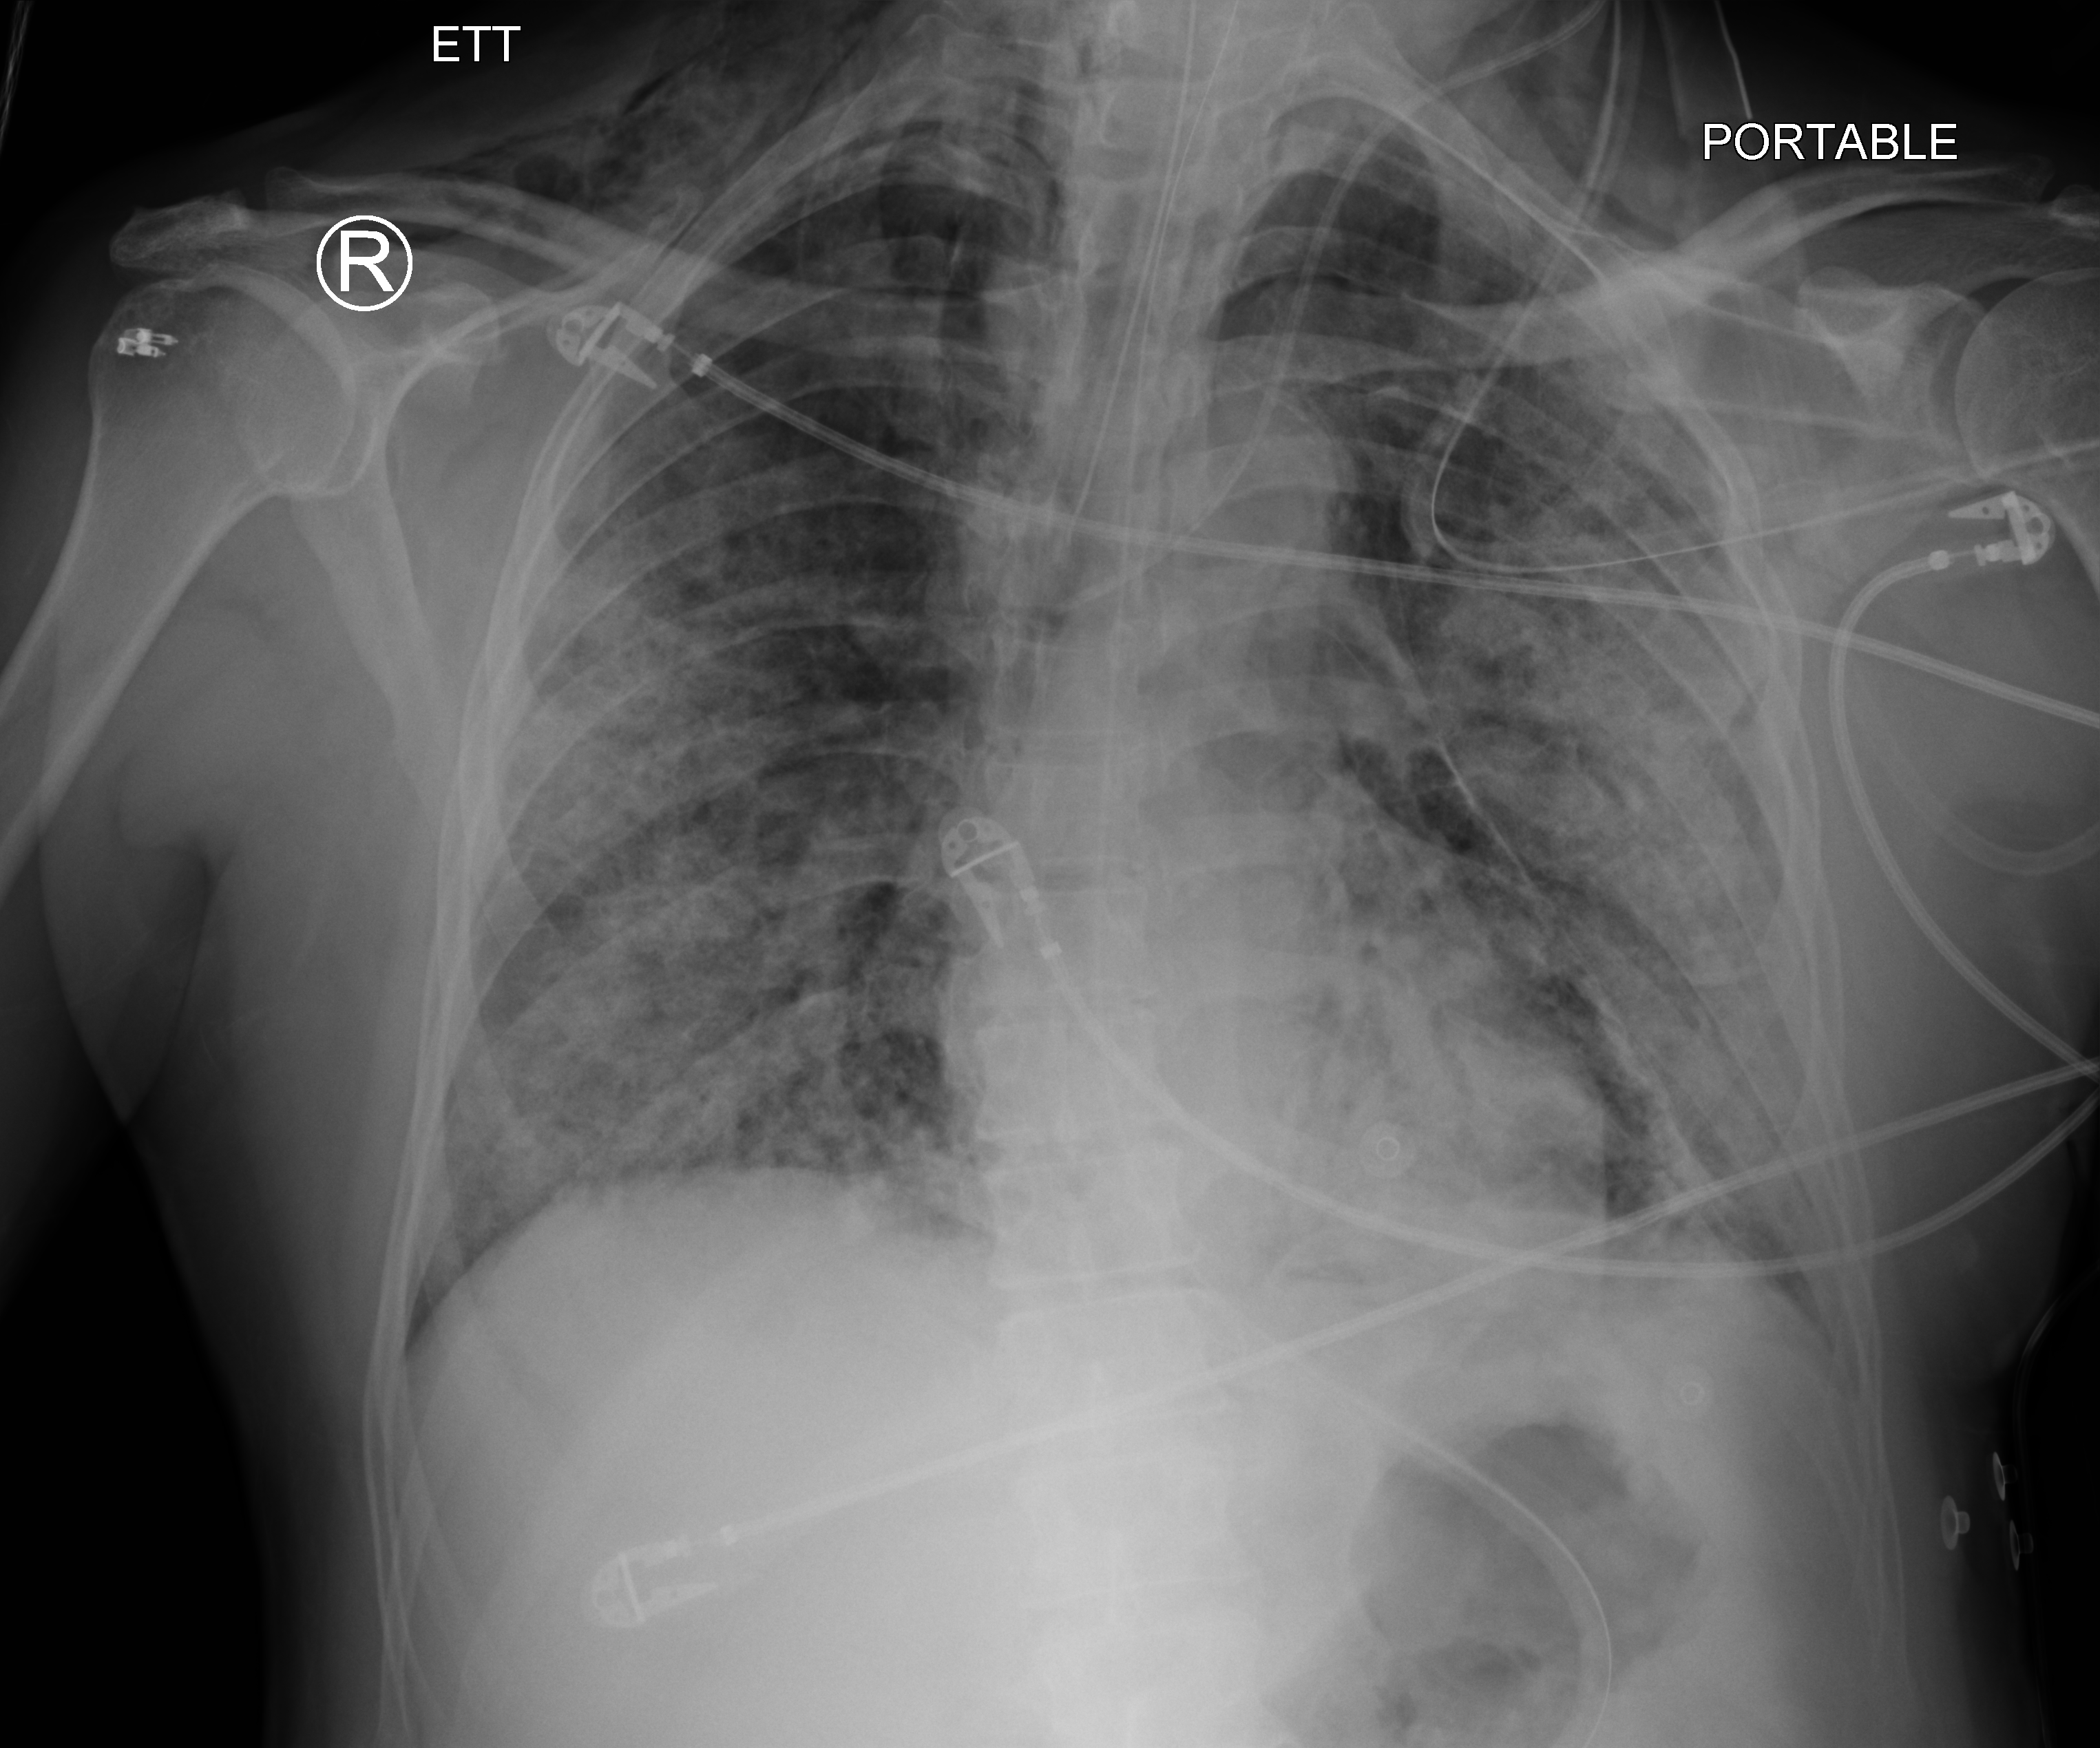
Bedside chest radiograph (computed radiography); anteroposterior (AP) projection. Male patient hospitalised with COVID-19, age 60–74 years.
Admission-level facts for this patient (not findings on this image; timing relative to this image not recorded): mechanically ventilated during this hospital stay: yes.